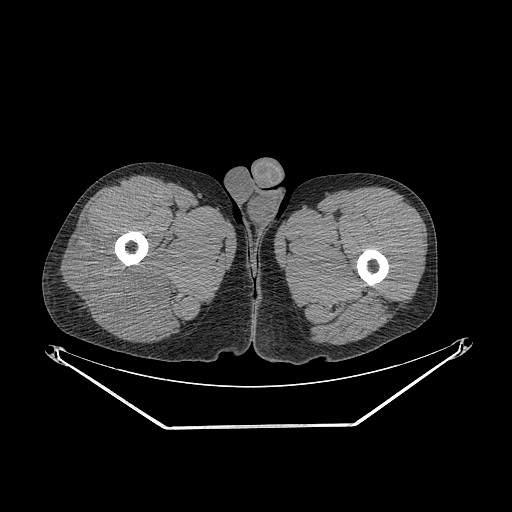
CT of an extremity soft-tissue mass (from a PET/CT study), one axial slice; position 266 of 267 along the scan axis; reconstruction kernel STANDARD; soft-tissue window (W 400 / L 40 HU); 3.75 mm slice thickness; 512 × 512 image matrix, field of view 500 × 500 mm. Male patient. From the clinical record (not read from this slice): histological type: poorly differentiated synovial sarcoma; grade: high; site of the primary tumour: right buttock.
Annotated regions visible in this slice (expert contour drawn on MRI and transferred to this co-registered scan by the dataset authors):
- gross tumour volume including surrounding oedema: bounding box (x1, y1, x2, y2) in pixels: (62, 228, 179, 334)
- gross tumour volume (mass): (62, 228, 165, 334)